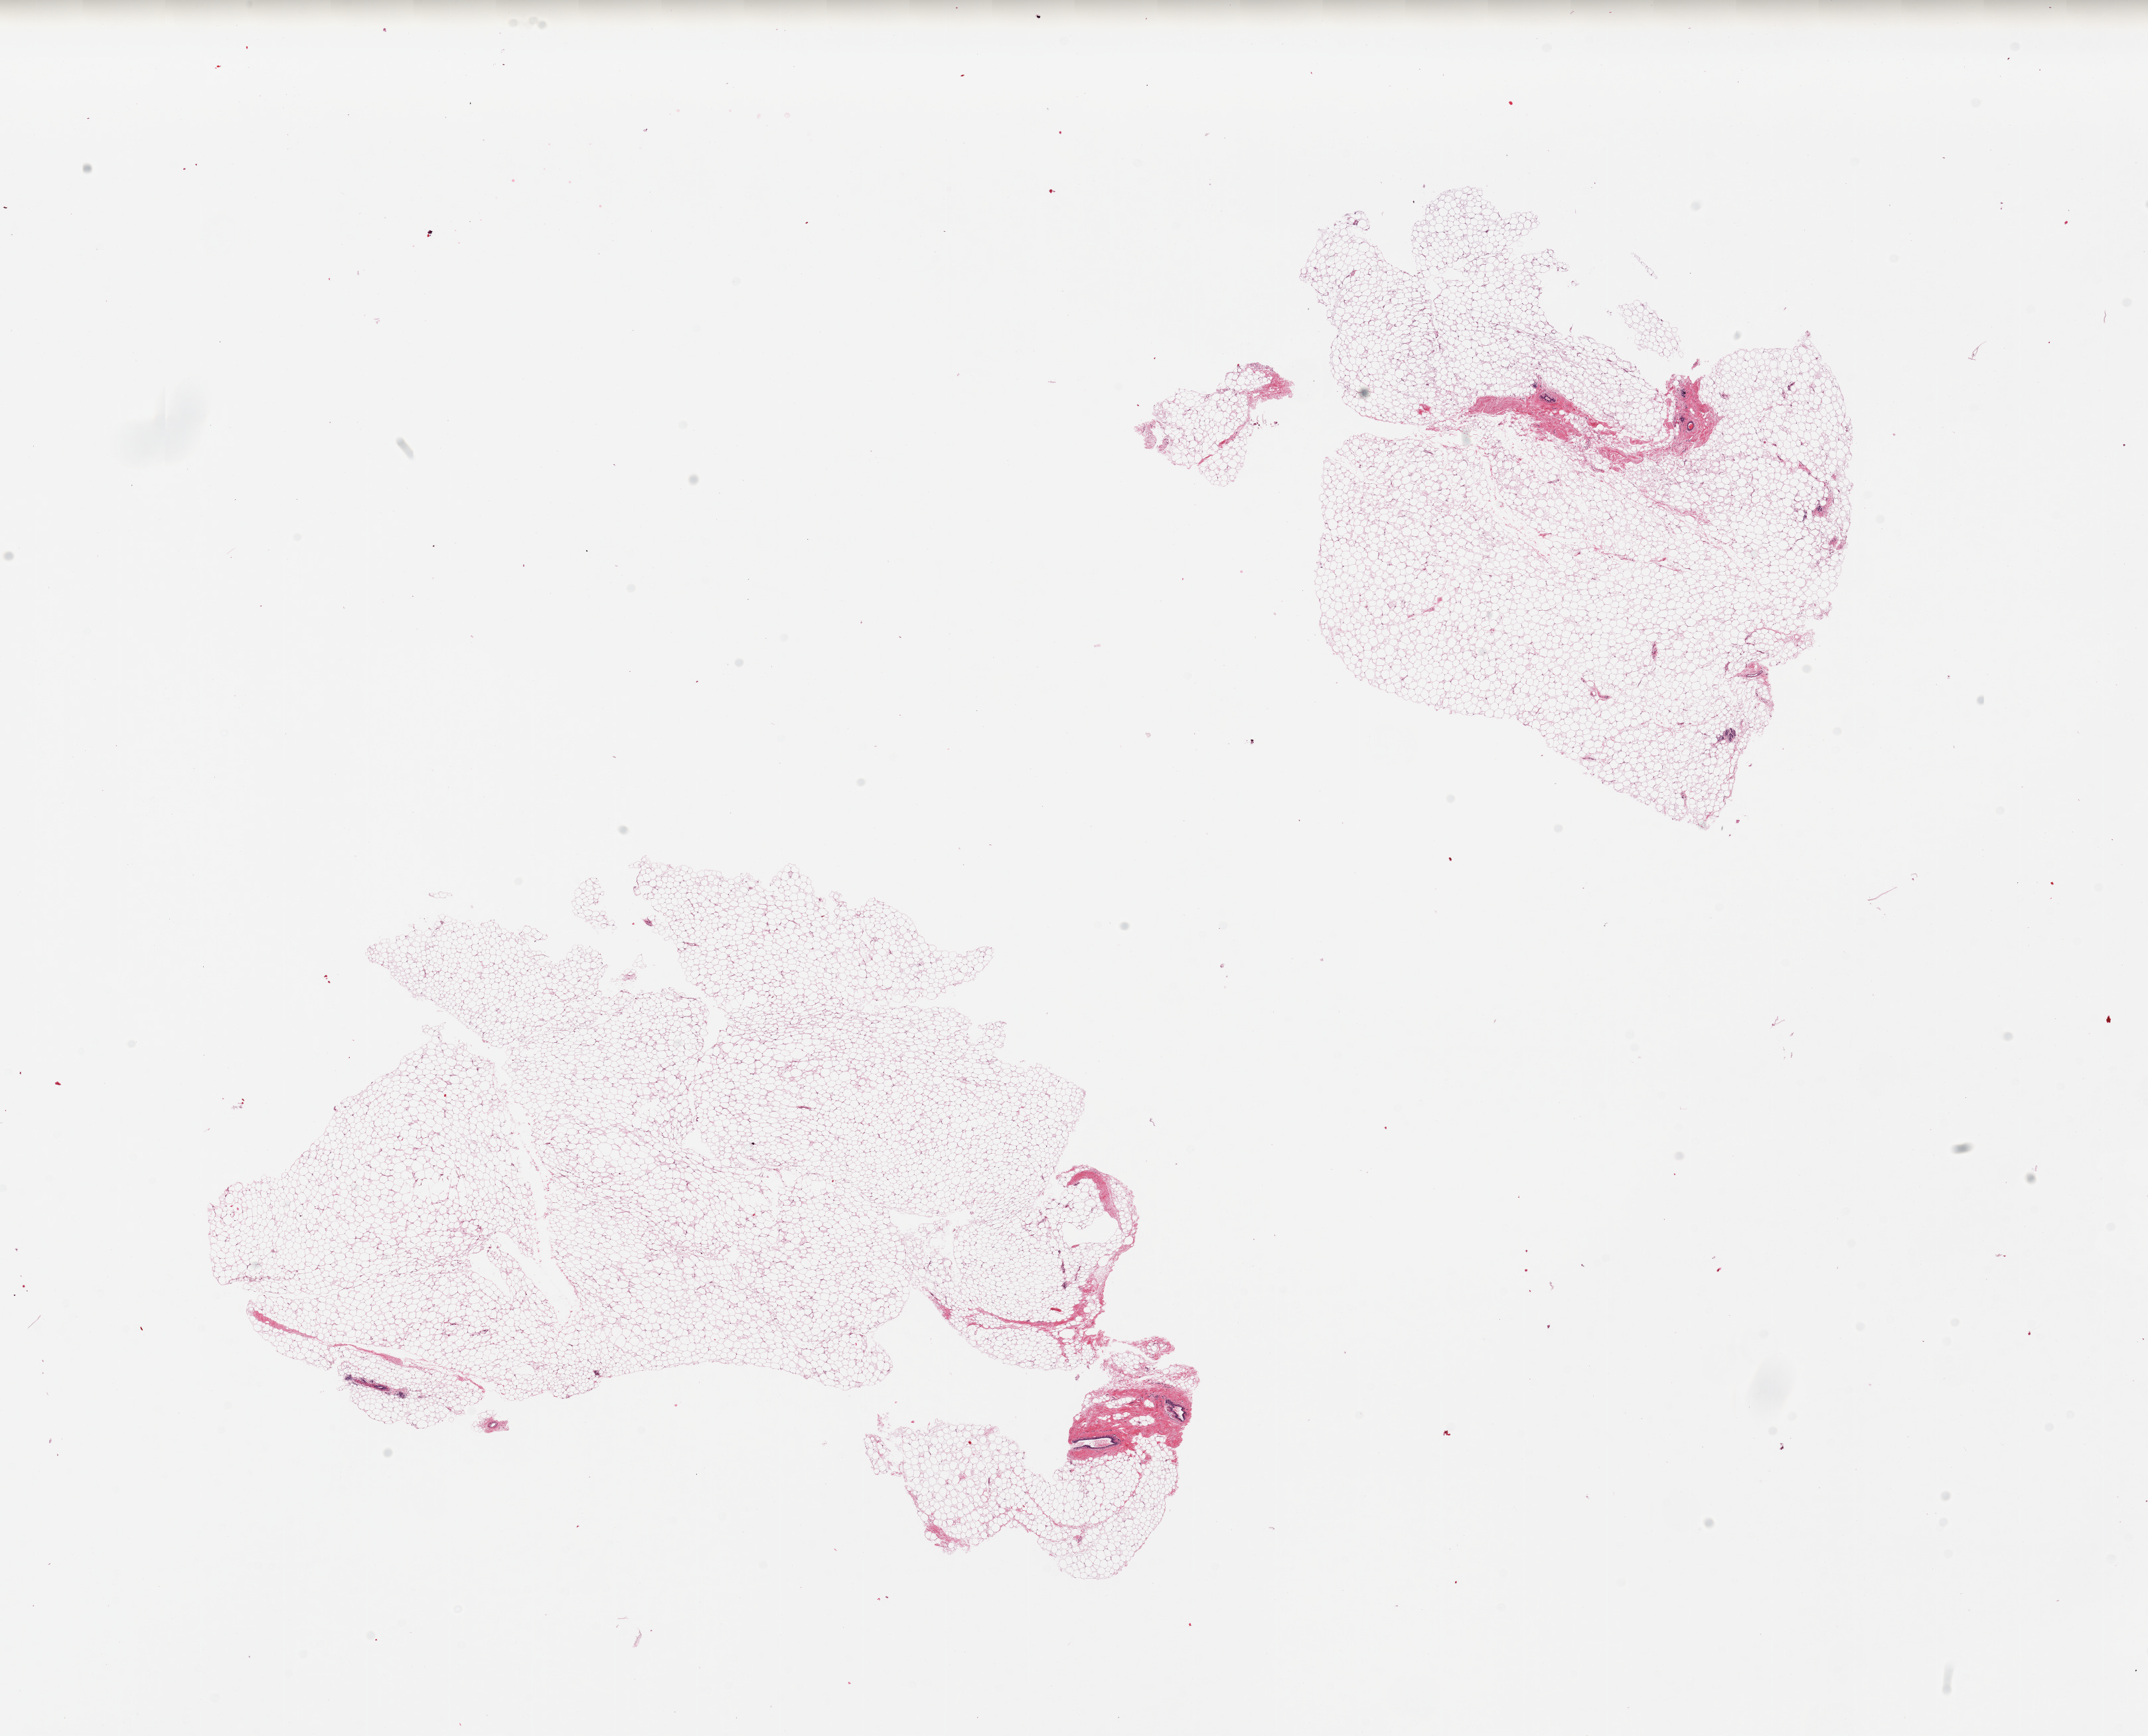
Whole-slide image, haematoxylin and eosin stain, brightfield, a low-resolution overview of the entire scanned area, about 25.6 x 20.7 mm (slide scanned at 20x). PAXgene-fixed, paraffin-embedded tissue. Section of breast (target tissue). Donor tissue sample. Donor: female.
Reviewer comment on this tissue sample: 2 pieces, largely adipose stroma; few ductal/lobular elements, atrophic, are present.